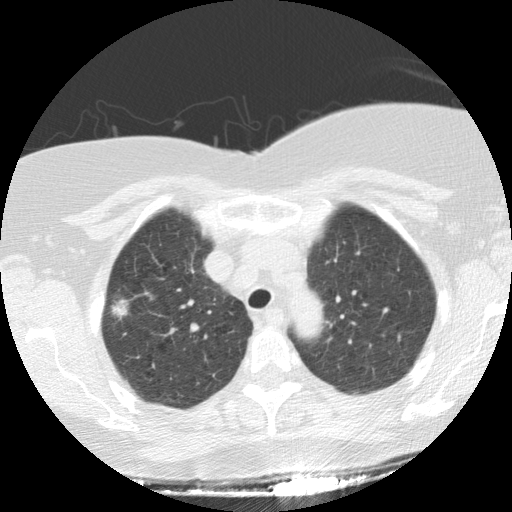
Low-dose screening chest CT, axial slice. First (baseline) screen. Lung window (W 1500 / L -600 HU). 2.5 mm slice thickness. Standard (soft-tissue) reconstruction kernel (STANDARD). 512 × 512 image matrix. Female, age 64 years at enrolment. Current smoker at enrolment.
Expert-annotated lung lesion, bounding box <91,273,143,333> (left, top, right, bottom; pixels). Screening reader's record for this exam (one nodule recorded; not confirmed to be the boxed lesion): non-calcified nodule or mass ≥4 mm, right upper lobe, 17 × 16 mm, spiculated (stellate) margins, soft tissue attenuation. Later outcome: lung cancer diagnosed 70 days after this screen — adenocarcinoma, NOS, right upper lobe, stage IIIA (AJCC 6th edition), 15 mm at pathology.